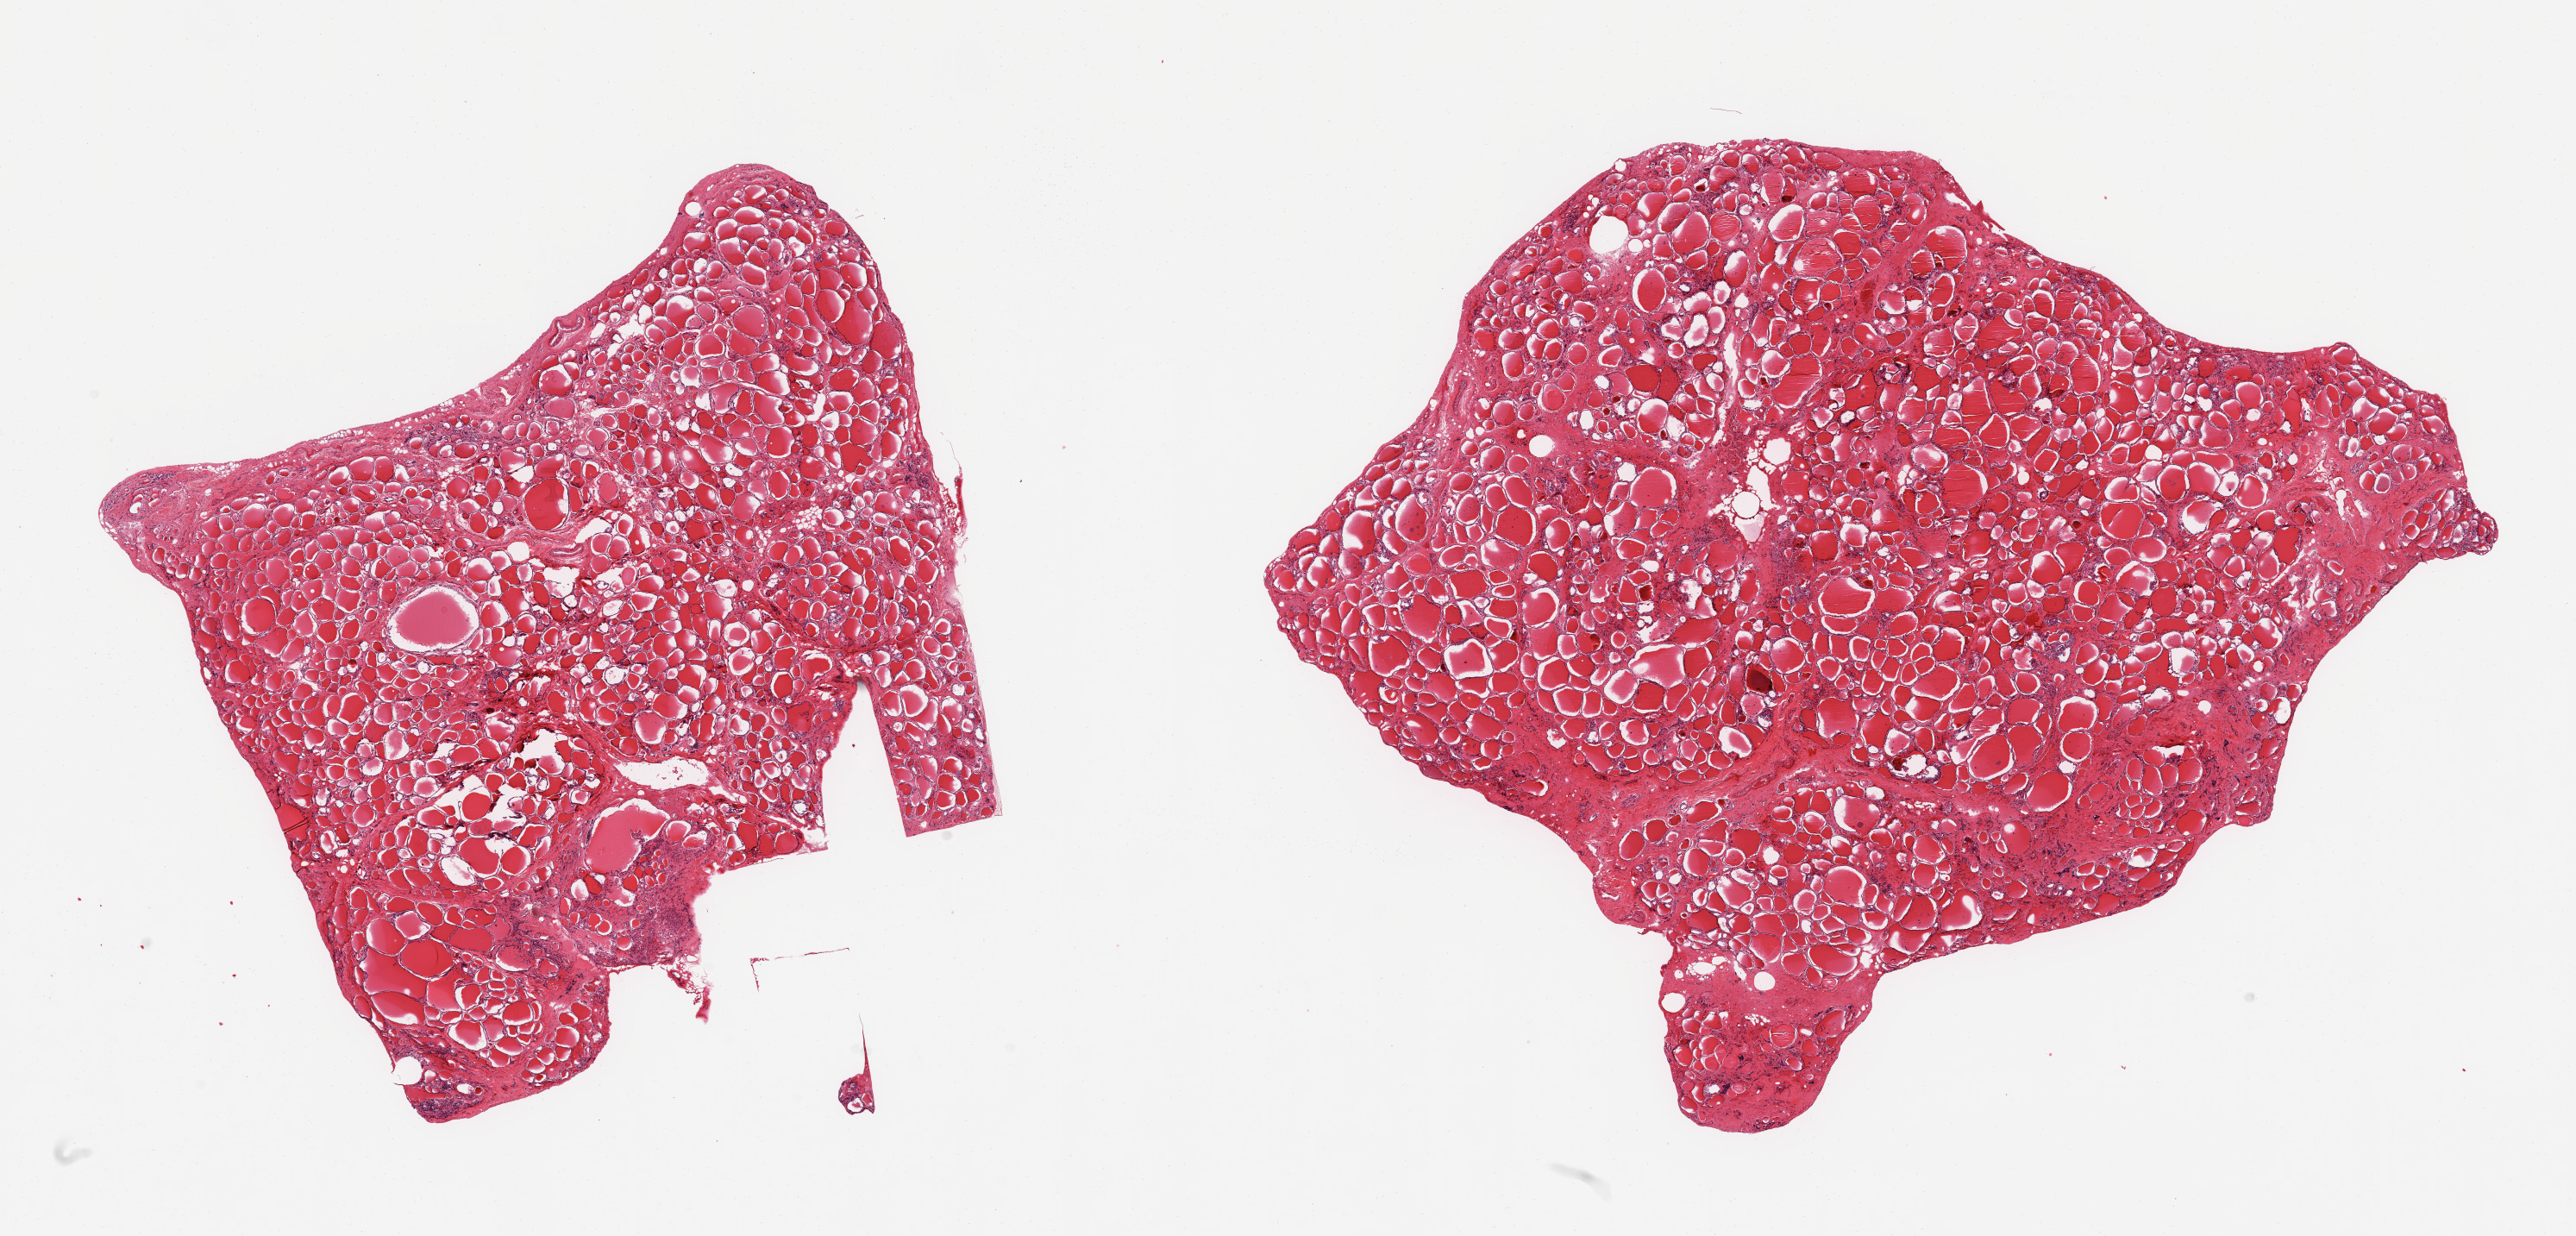
Haematoxylin and eosin whole-slide image — shown as a low-resolution overview of the whole scanned area (about 23.6 x 11.3 mm, from a 20x scan). PAXgene-fixed, paraffin-embedded tissue. Target tissue: thyroid. Tissue donor sample. Donor sex: female.
• review note (as recorded): 2 pieces; 5% fibrous content